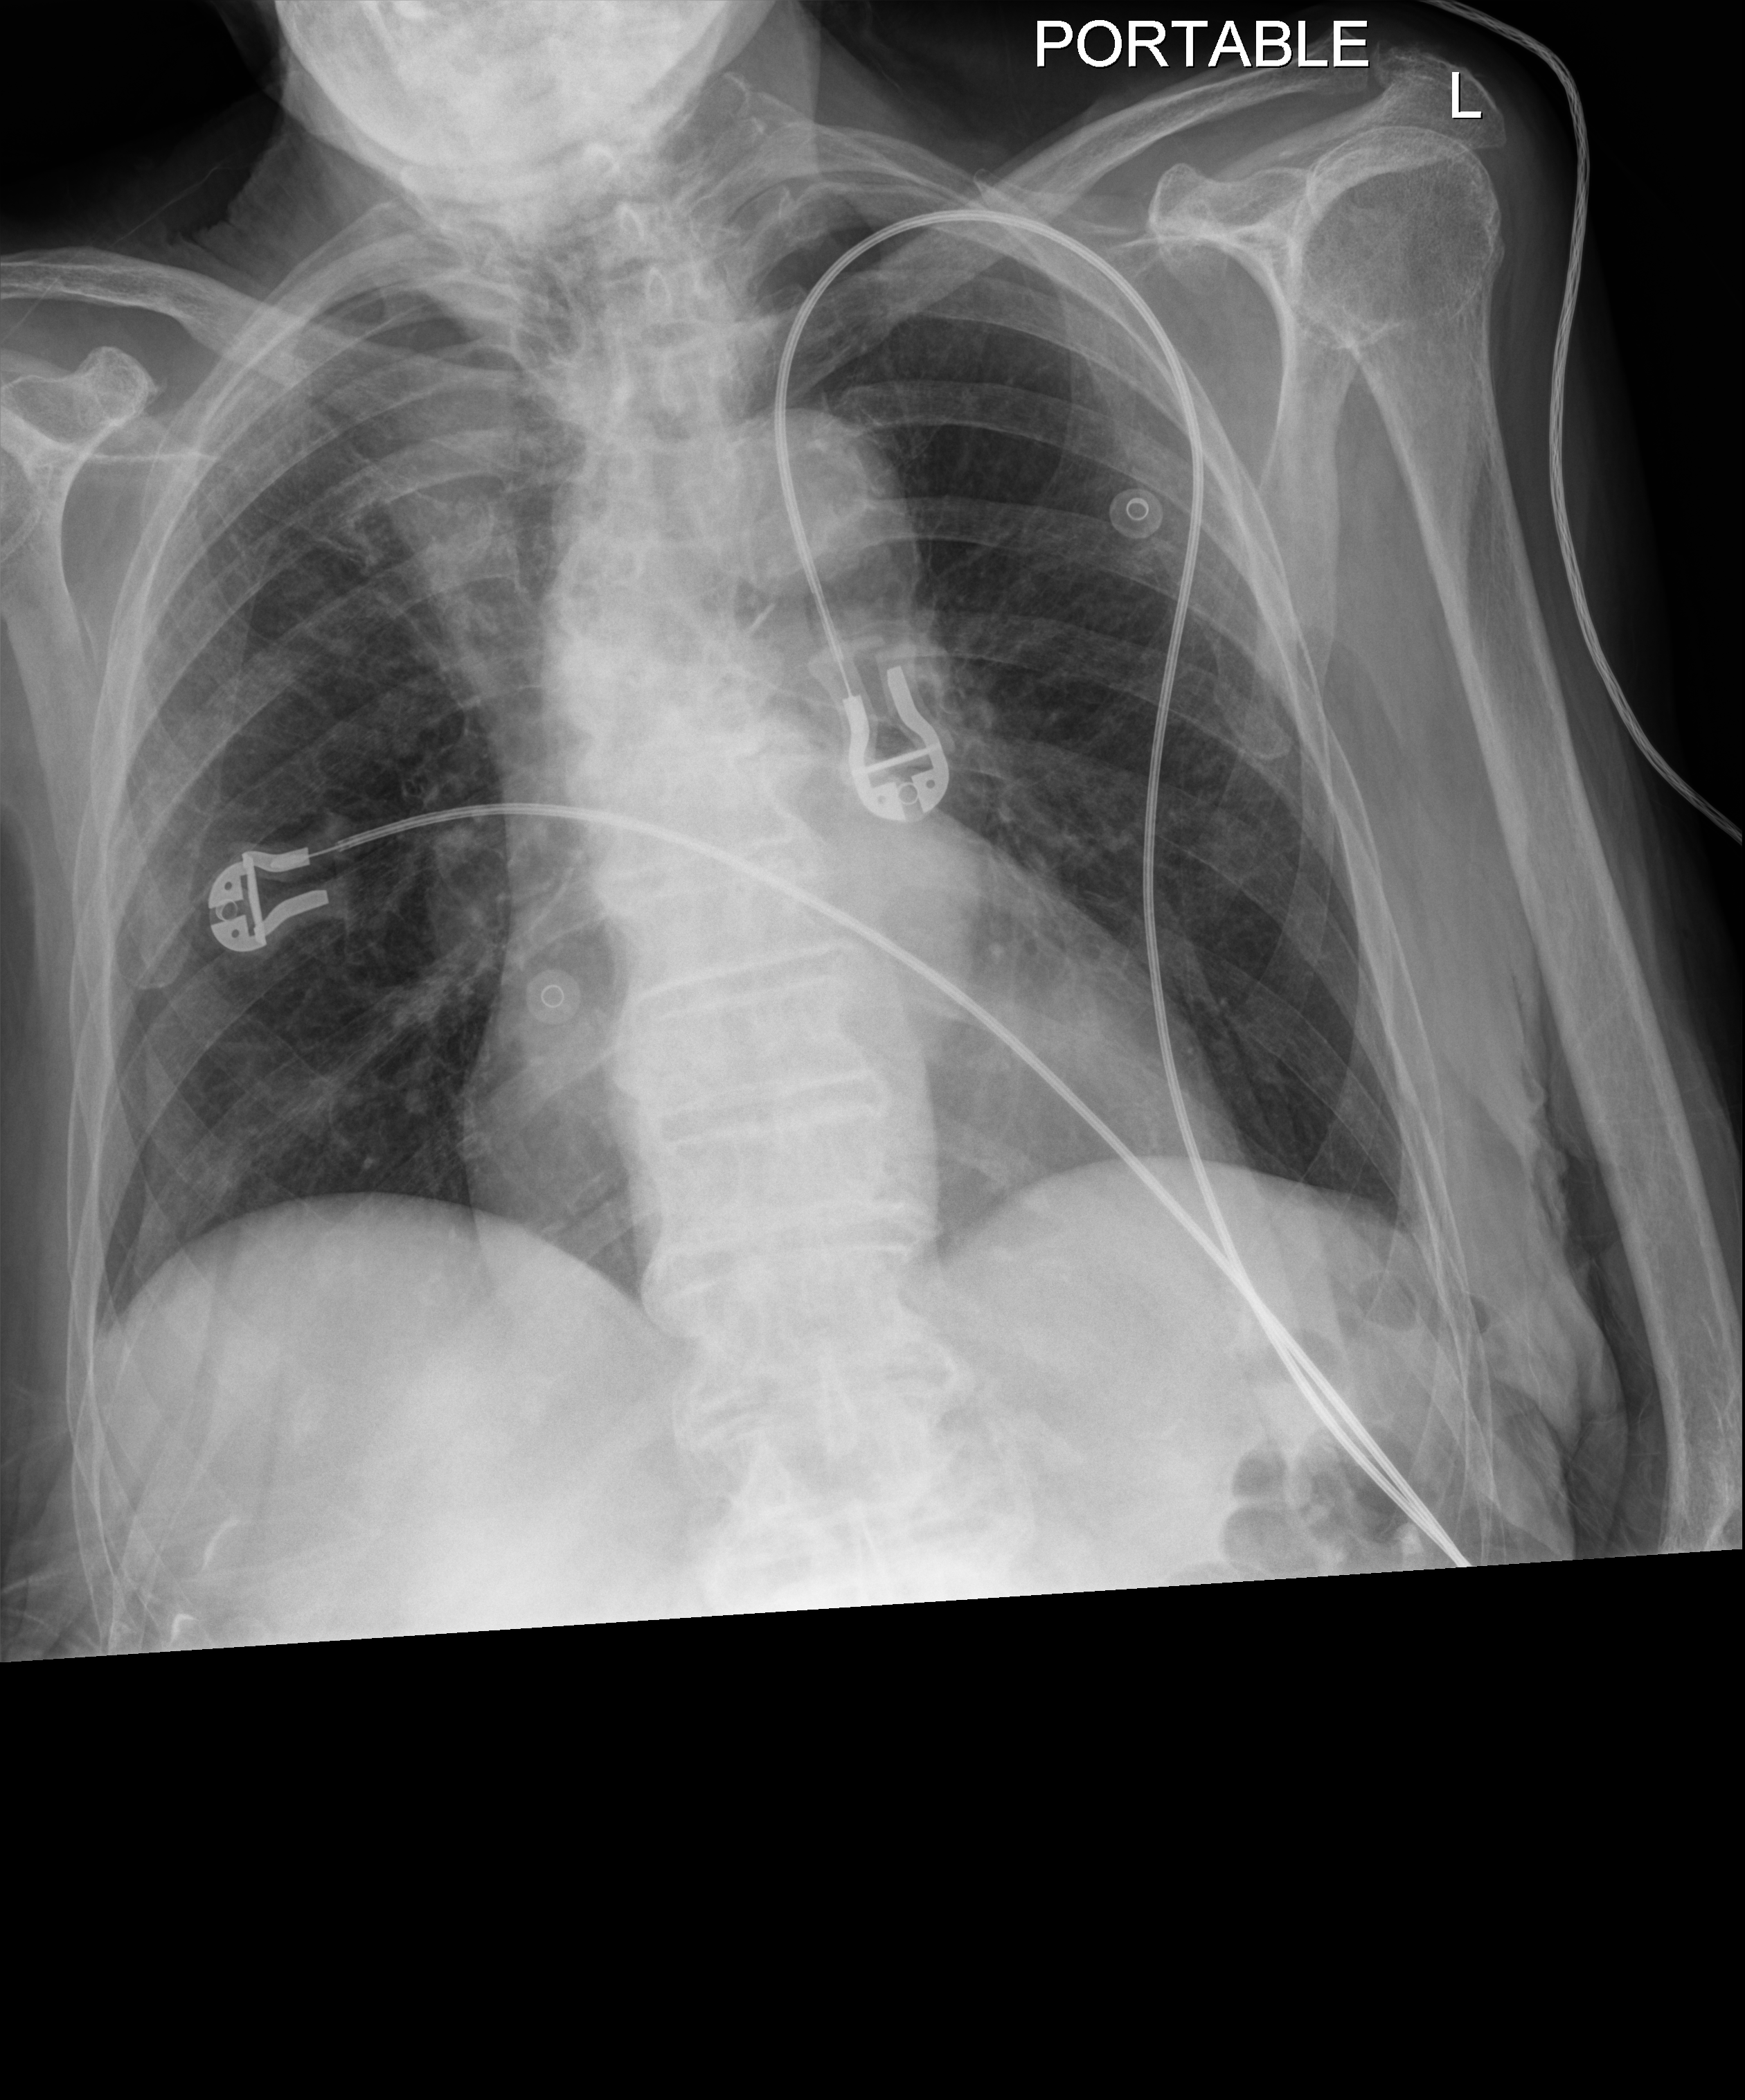
Chest X-ray. Patient hospitalised with COVID-19; female, aged 75–90 years.
Admission-level facts for this patient (not findings on this image; timing relative to this image not recorded): mechanically ventilated during this hospital stay: no; admitted to intensive care during this hospital stay: no.